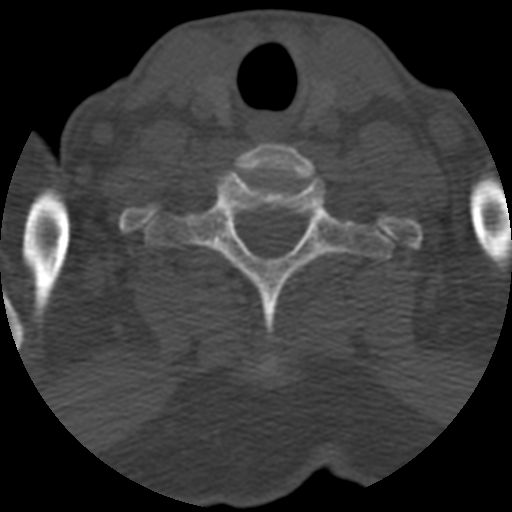
CT including the spine, one axial slice. Slice 521 of 708 in the series (ordered by position). 120 kVp. One of 3 acquisitions stored at this slice position. Bone window (W 1800 / L 400 HU). 512 × 512 image matrix, field of view 160 × 160 mm. Patient age 55 years. Case-level facts recorded for this patient, not image findings: primary cancer: colon.
Annotated regions visible in this slice (semi-automatic segmentation, software-assisted and operator-edited):
- T1 vertebra: box from (x=145, y=167) to (x=391, y=376) px